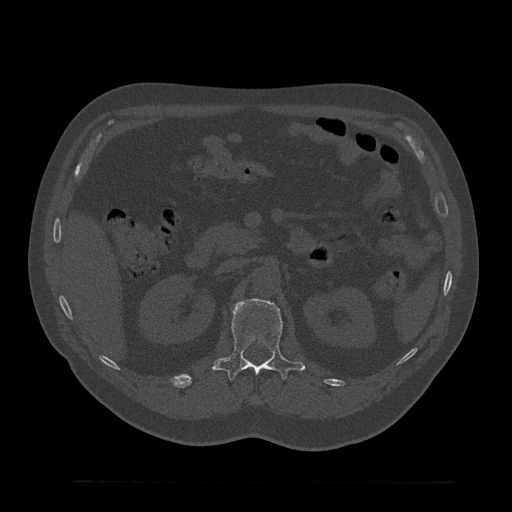
CT including the spine, one axial slice. Position 170 of 797 along the scan axis. Reconstruction kernel Br40s/3. Bone window (W 1800 / L 400 HU). 0.5 mm slice thickness. 512 × 512 image matrix. Patient: male, 61 years. From the clinical record (not read from this slice): primary cancer: prostate.
Annotated regions visible in this slice (semi-automatic segmentation, software-assisted and operator-edited):
- L1 vertebra: bounding box (x1, y1, x2, y2) in pixels: (212, 299, 305, 381)